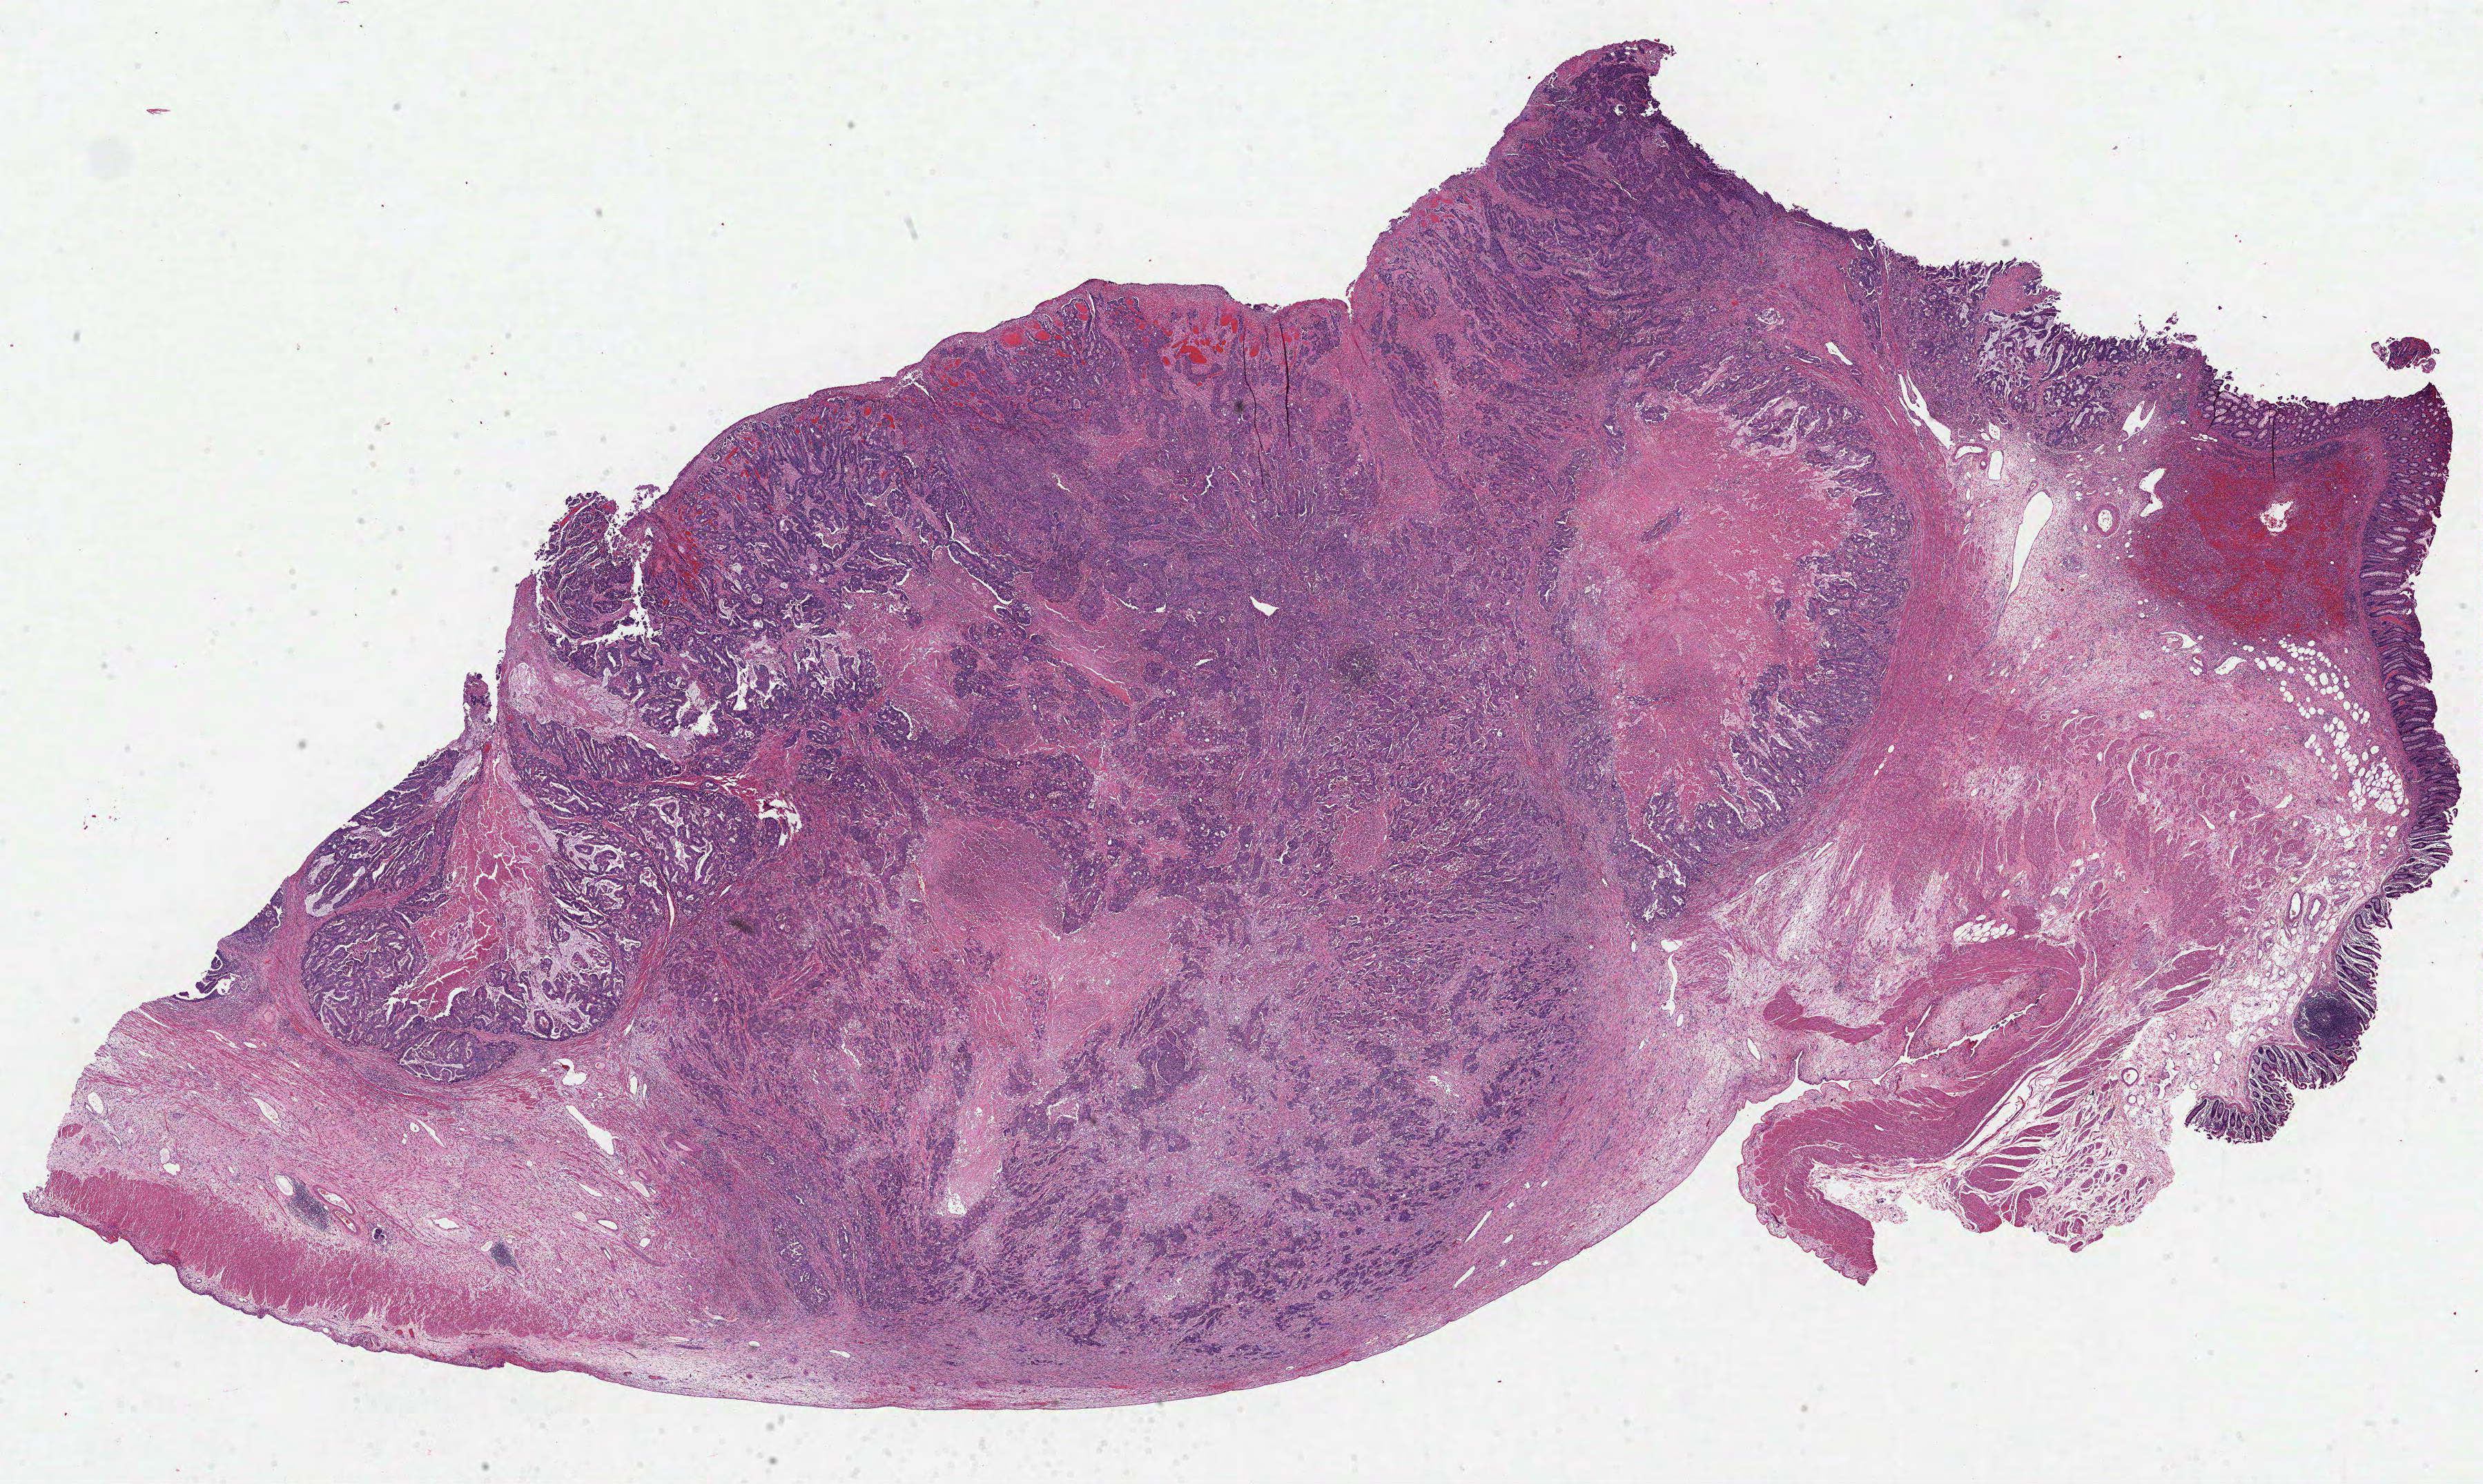
H&E whole-slide image, whole scanned area (about 29.0 x 17.3 mm, acquisition: 40x scan) shown as a low-resolution overview; formalin-fixed paraffin-embedded (FFPE) diagnostic section; sample: primary tumour, colon. Patient: female, age at initial diagnosis 71 years.
* histologic diagnosis: Adenocarcinoma, NOS (cecum)
* AJCC pathologic stage: IVA
* TNM: T4a N1 M1
* lymph nodes positive (case pathology): 2 of 4 examined